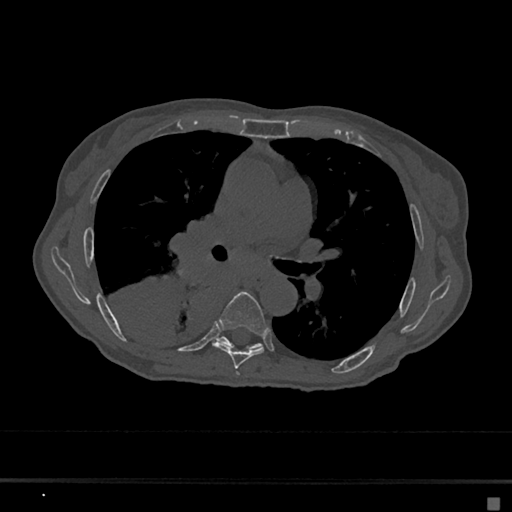
CT including the spine, one axial slice. Slice 404 of 797 in the series (ordered by position). Reconstruction kernel Br40s/3. Bone window (W 1800 / L 400 HU). 0.5 mm slice thickness. 512 × 512 image matrix, field of view 360 × 360 mm. Patient: female, 68 years. Case-level facts recorded for this patient, not image findings: primary cancer: renal.
Structures marked on this image (semi-automatically segmented with operator editing):
- T5 vertebra: bounding box [x1, y1, x2, y2] px = [236, 372, 240, 375]
- T6 vertebra: [213, 291, 269, 369]
- T7 vertebra: [217, 337, 262, 349]